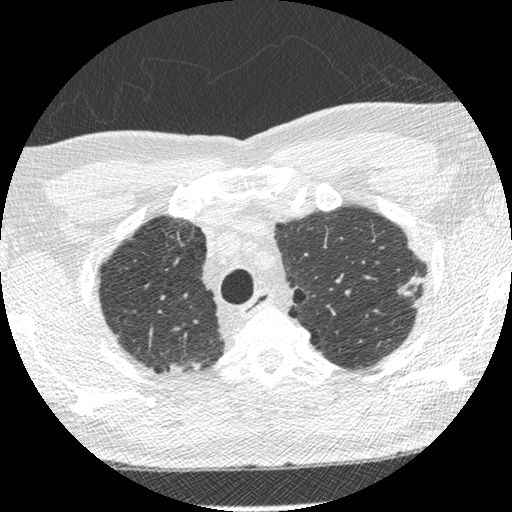
Low-dose screening chest CT, one axial slice. Position 236 of 275 along the scan axis. Reconstruction kernel STANDARD. 120 kVp. Lung window (W 1500 / L -600 HU). 512 × 512 image matrix, field of view 330 × 330 mm.
Structures marked on this image (outlined manually by an expert reader):
- lesion 1 (tumor, upper lobe of left lung): box from (x=398, y=276) to (x=424, y=296) px